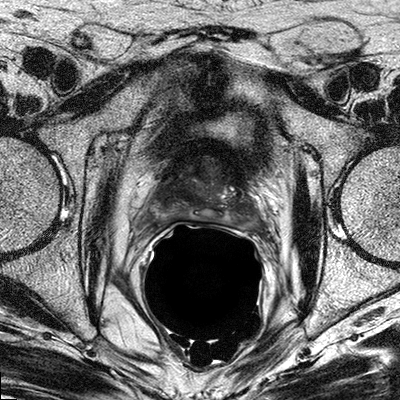
Multiparametric prostate MRI examination; 3 images, each a single mid-volume slice chosen by position (not for content).
Image 1: T2-weighted axial slice, slice 17 of 32, 3 mm slice thickness.
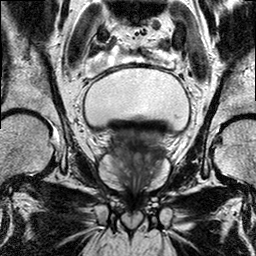
Image 2: coronal T2-weighted image, series "T2W_TSE_COR", slice 13 of 24.
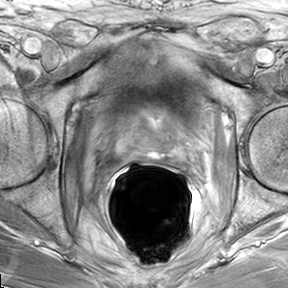
Image 3: DCE (dynamic gadolinium-enhanced) axial slice, slice 17 of 32, dynamic phase 5 of 8.
Report of this MRI examination:
Prostate has a maximal lateral diameter of 5.2 cm, a maximal craniocaudal diameter of 3.6 cm and a maximal AP diameter of 2.8 cm resulting in an estimated gland volume of 27 cc. The zonal anatomy is preserved. In the mid third of the prostate, in the anterior aspect of the right paramedian central gland, at 11 o'clock, there is a irregular 13 x 14 mm area of suspicious enhancement, suggestive for malignancy (series 701 slice location 27-36). On the T2-W images the mass abuts the fibromuscular band and there is asymmetric bulging. There is also suspicious enhancement beyond the deviated fibromuscular band in this location. Beginning extraprostatic extension very likely. Series 501 slice location 33-36. The peripheral zones show no evidence of malignancy. No evidence for involvement of the neurovascular bundle on either side. The seminal vesicles and show diffuse low signal on the T2 weighted images; however the anatomy of the seminal vesicles with thin walls and regular vesicles seems to be preserved; there is no suspicious enhancement seen within the vesicles or within the walls. Therefore this T2 hypo intensity most likely caused by radiation. Seminal vesicles infiltration unlikely. No evidence of involvement of bladder neck and rectal wall. No suspiciously enlarged obturator and iliac lymph nodes. IMPRESSION: 1) 1.4cm mass in the right anterior paramedian central gland, mid third of the prostate, as detailed above. Findings are highly suspicious for beginning extraprostatic extension (beyond the fibromuscular band) at 11 o'clock. 2) No evidence for involvement of the neurovascular bundle on either side. 3) No evidence of seminal vesicles infiltration. 4) No suspiciously enlarged obturator and iliac lymph nodes.